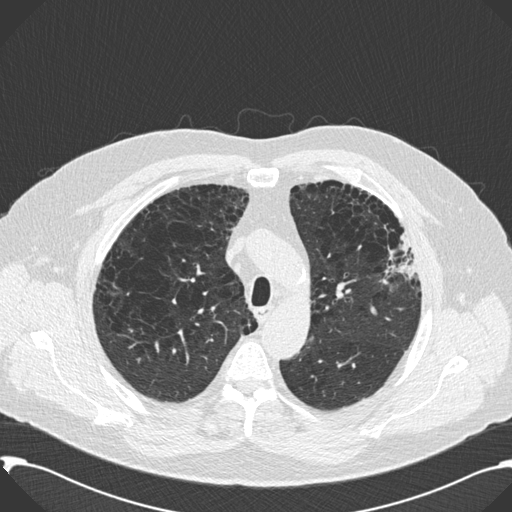
Chest CT (low-dose screening protocol), one axial image. Second annual screen. Lung window (W 1500 / L -600 HU). 2 mm slice thickness. Slice 46 of 199 in the series. 512 × 512 image matrix. Male, age 59 years at enrolment.
Expert reader's lesion annotation, bounding box <363,210,421,296> (left, top, right, bottom; pixels). No non-calcified nodule or mass ≥4 mm was recorded by the screening reader at this exam. Lung cancer was diagnosed 518 days after this screen (after the third annual screen): bronchiolo-alveolar carcinoma, mixed mucinous and non-mucinous, left upper lobe, stage IA (AJCC 6th edition), 20 mm at pathology.